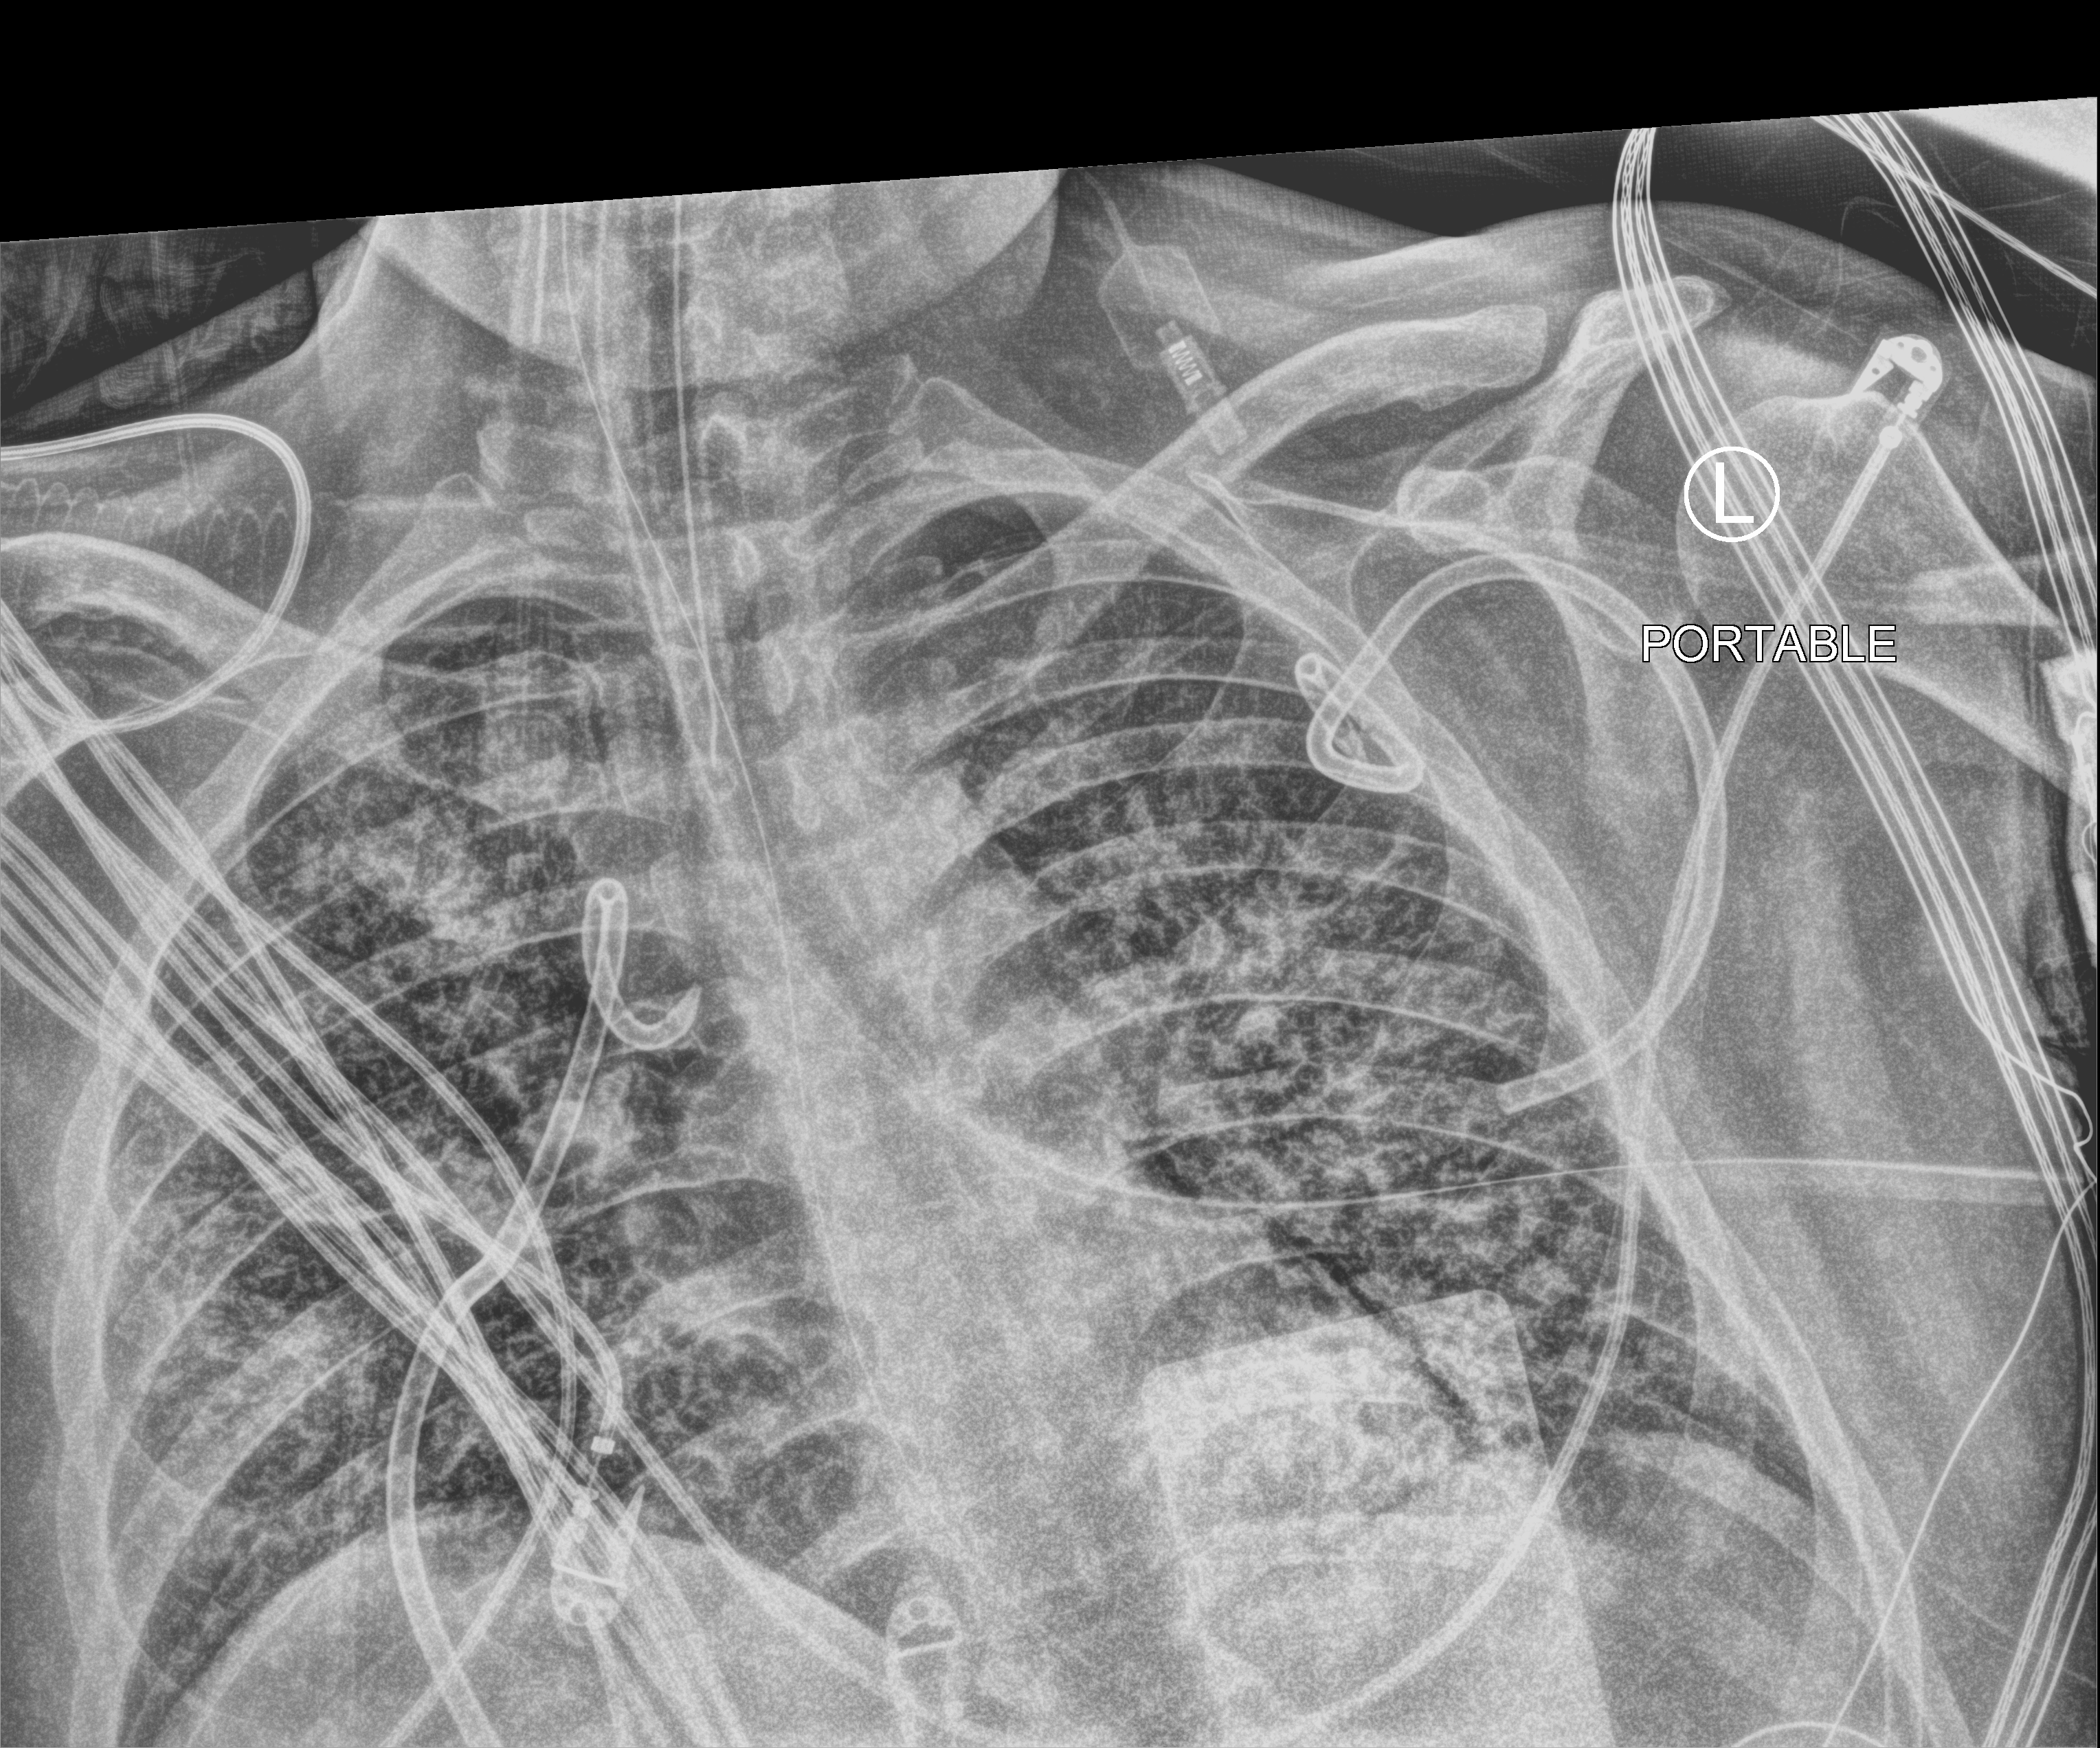
Chest X-ray (portable). Adult patient hospitalised with COVID-19, age 18–59 years.
From the hospital-stay record, not from the radiograph (when in the stay this image was taken is not recorded): admitted to intensive care during this hospital stay: yes; length of hospital stay: 31 days.